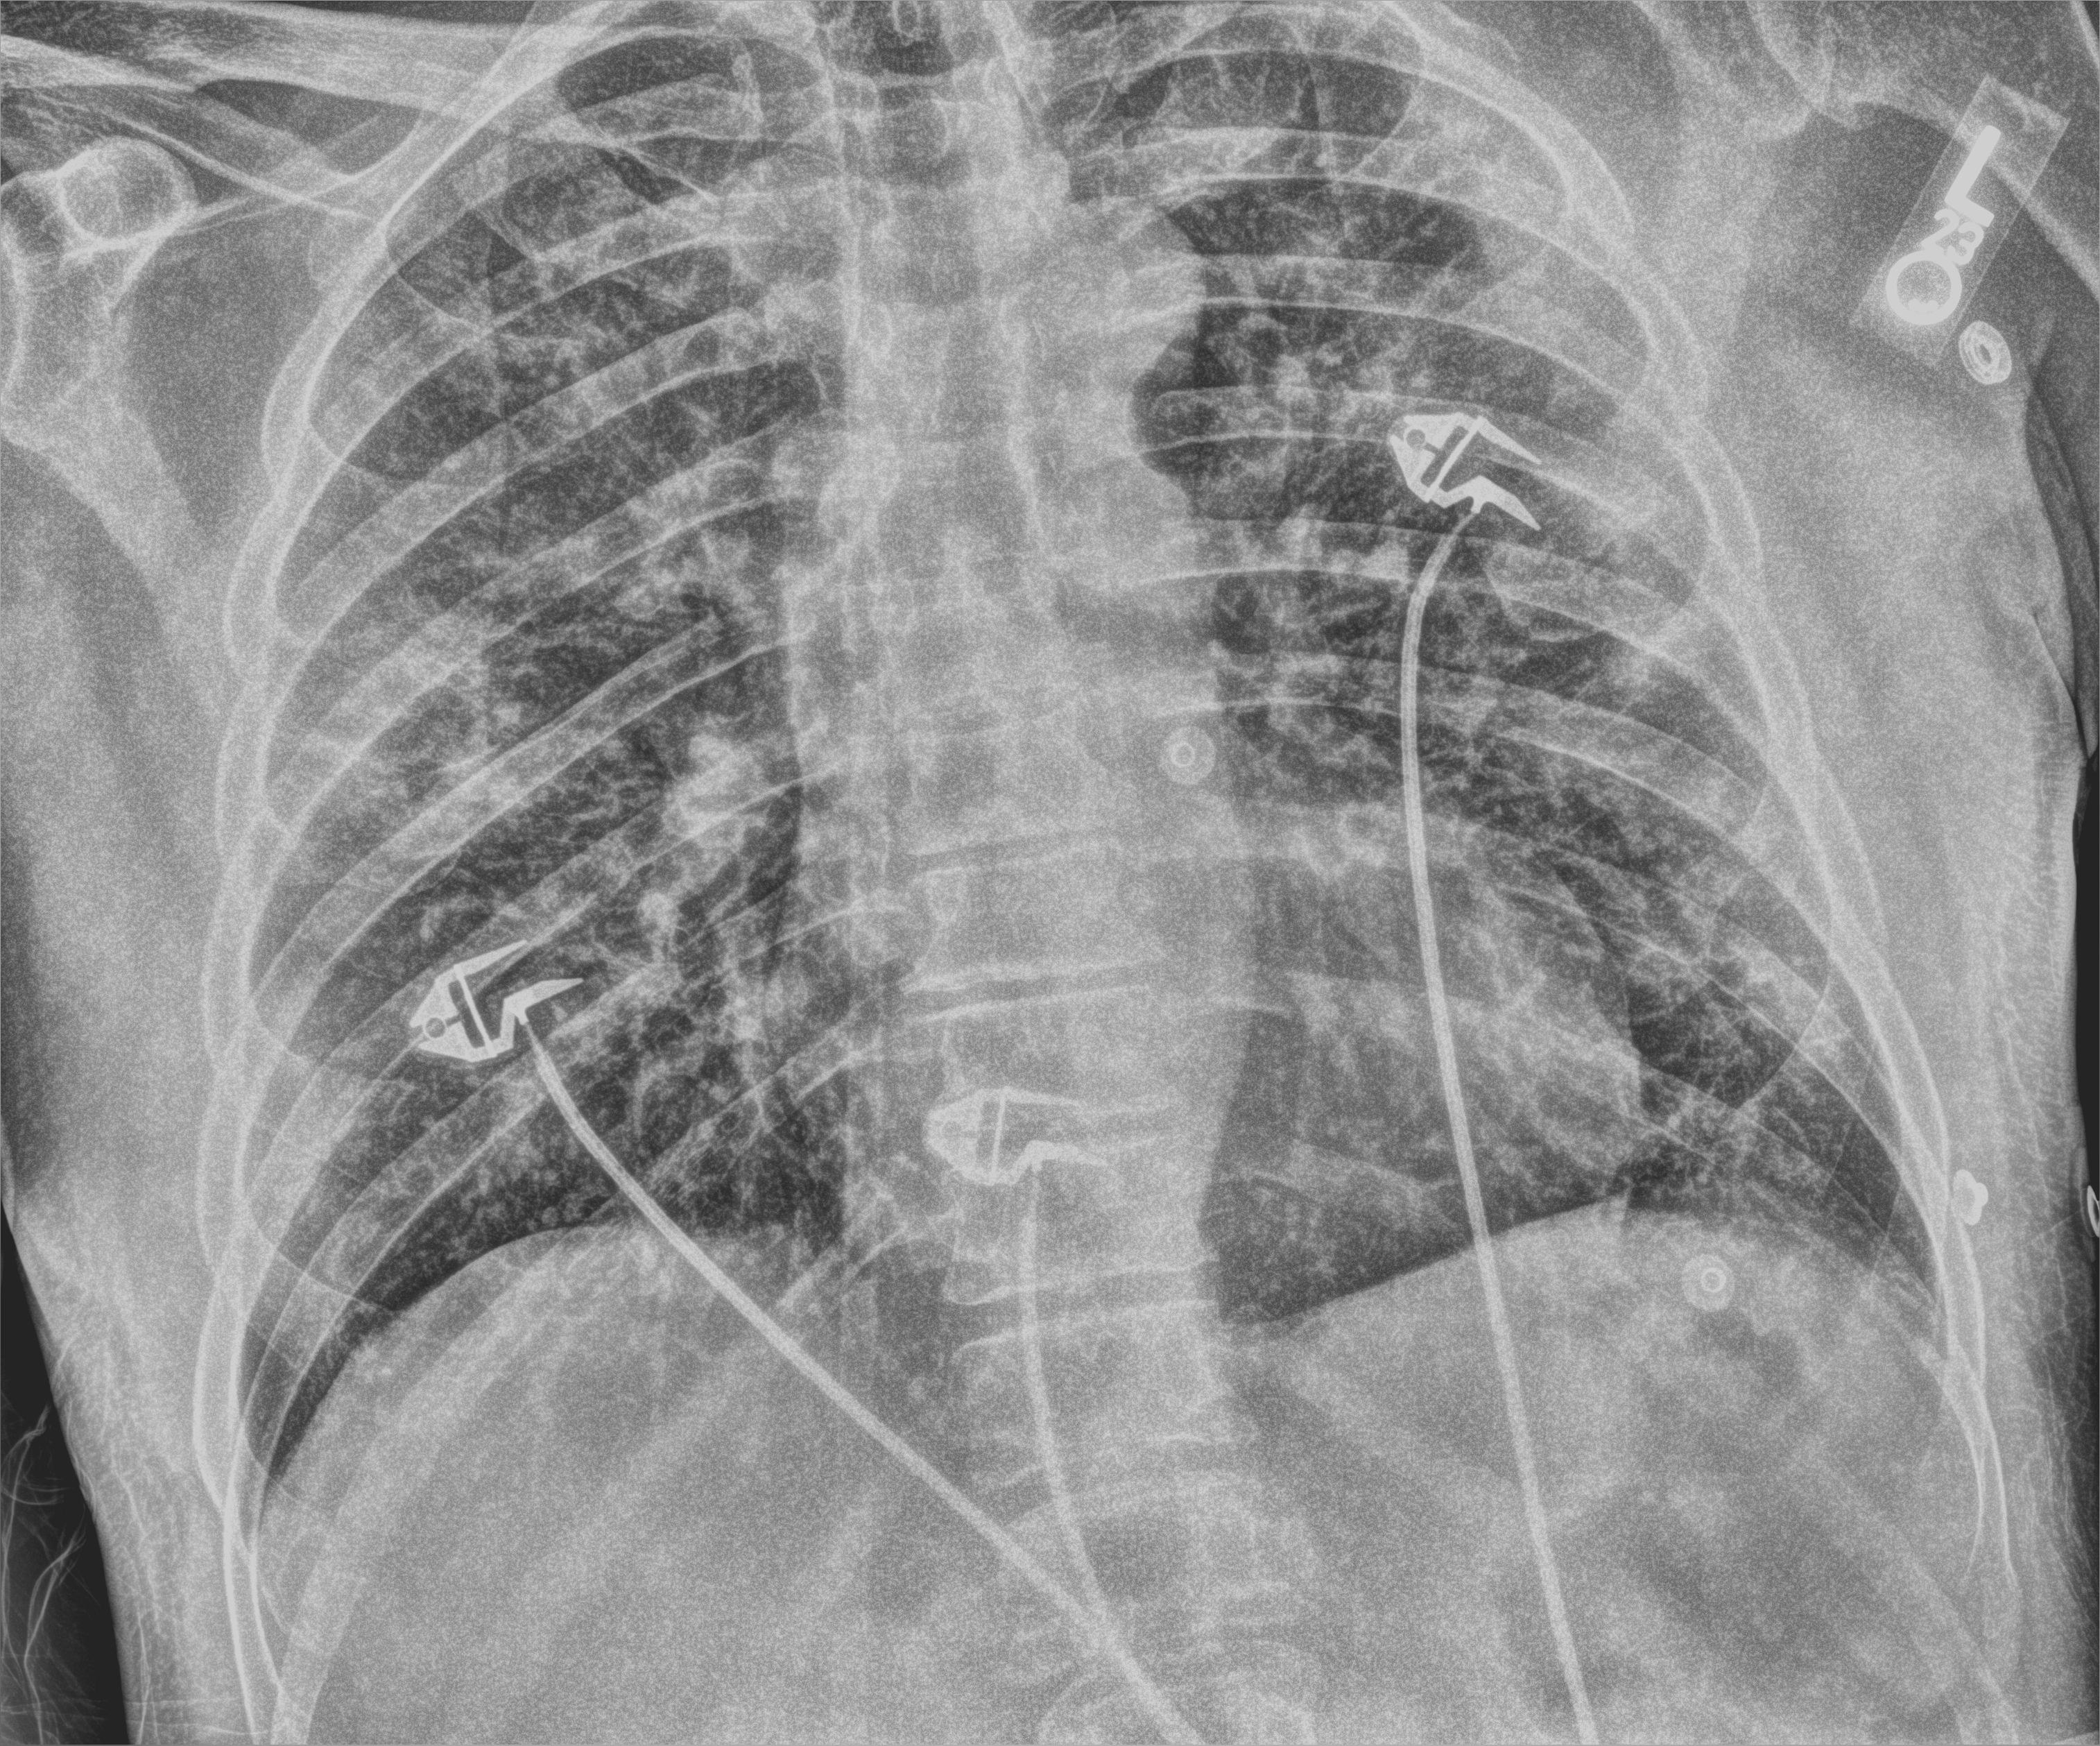
Portable chest radiograph; anteroposterior (AP) projection. Male patient hospitalised with COVID-19, age 18–59 years.
Hospital-stay facts (about this admission, not read from this image; timing relative to this image not recorded): admitted to intensive care during this hospital stay: no; chronic kidney disease (admission record): no.